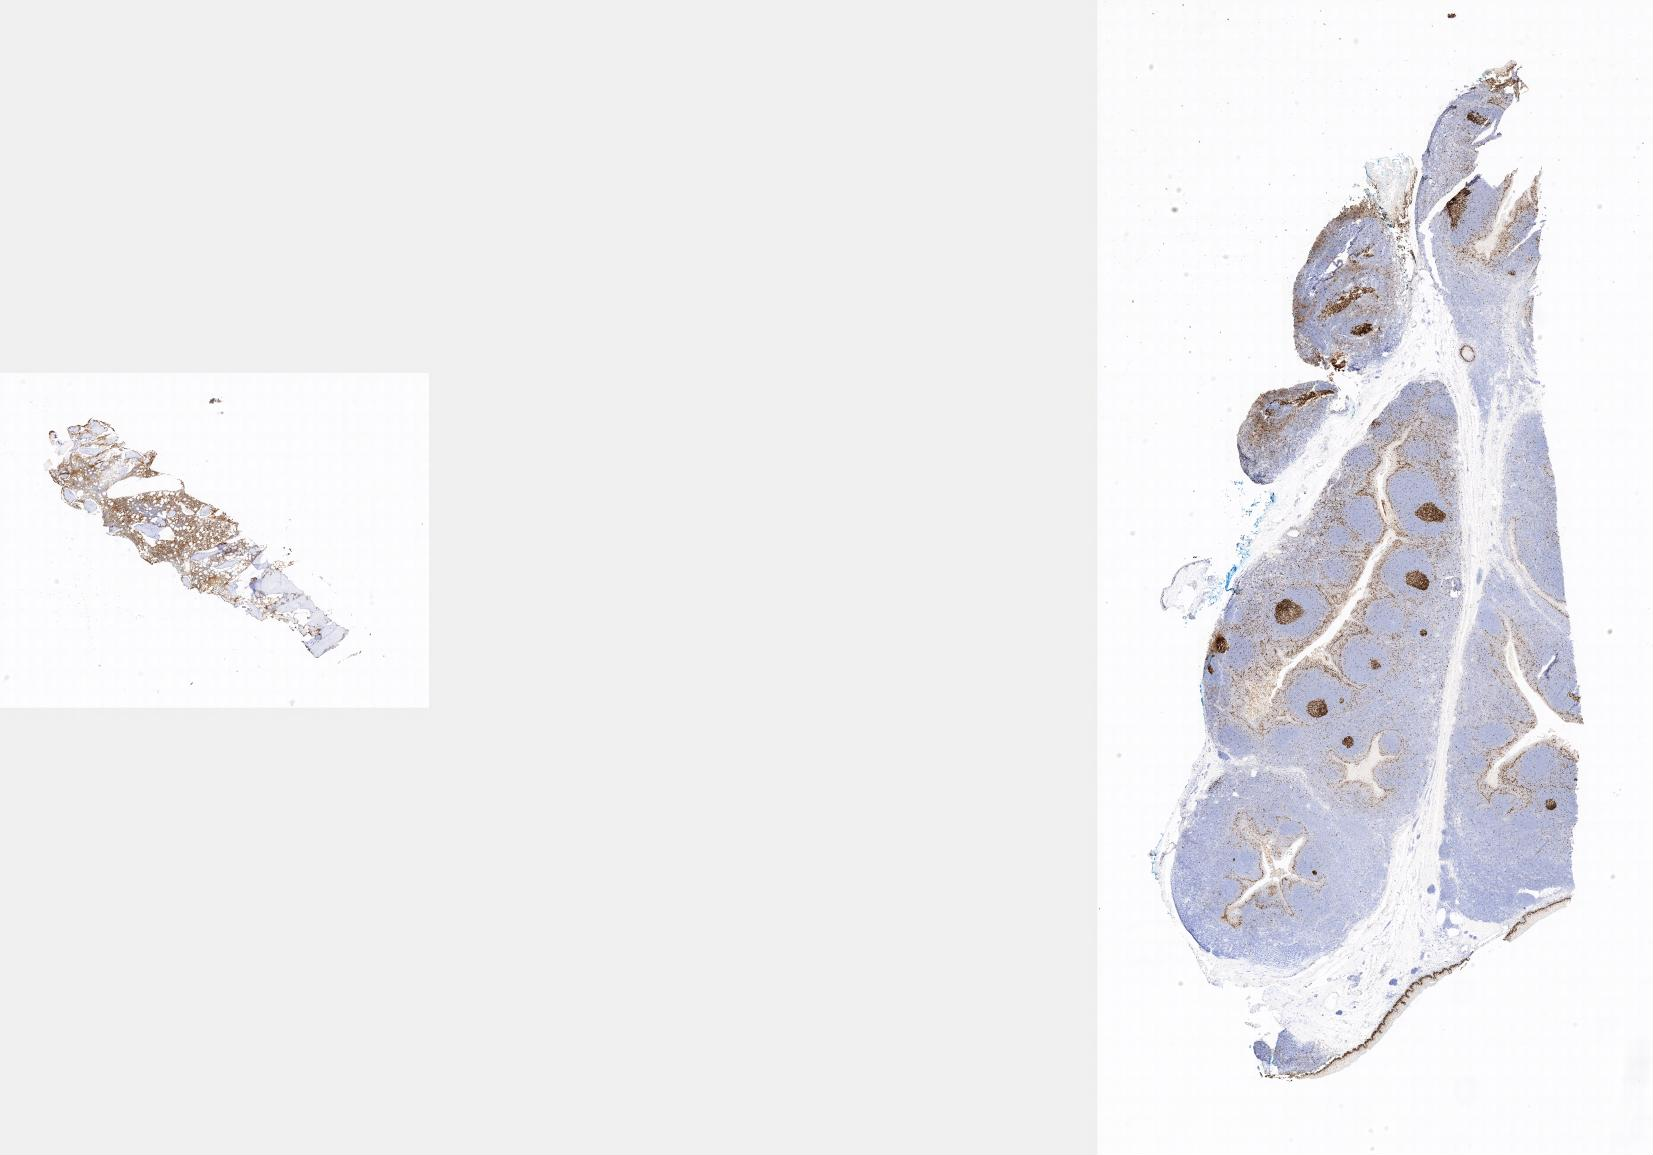
Immunohistochemistry (IHC) whole-slide image stained for Ki-67 — shown as a low-resolution overview of the whole scanned area. Tumor tissue. Site: bone marrow. Patient: female, age at initial diagnosis 4 years.
Diagnosis: Burkitt lymphoma, NOS.